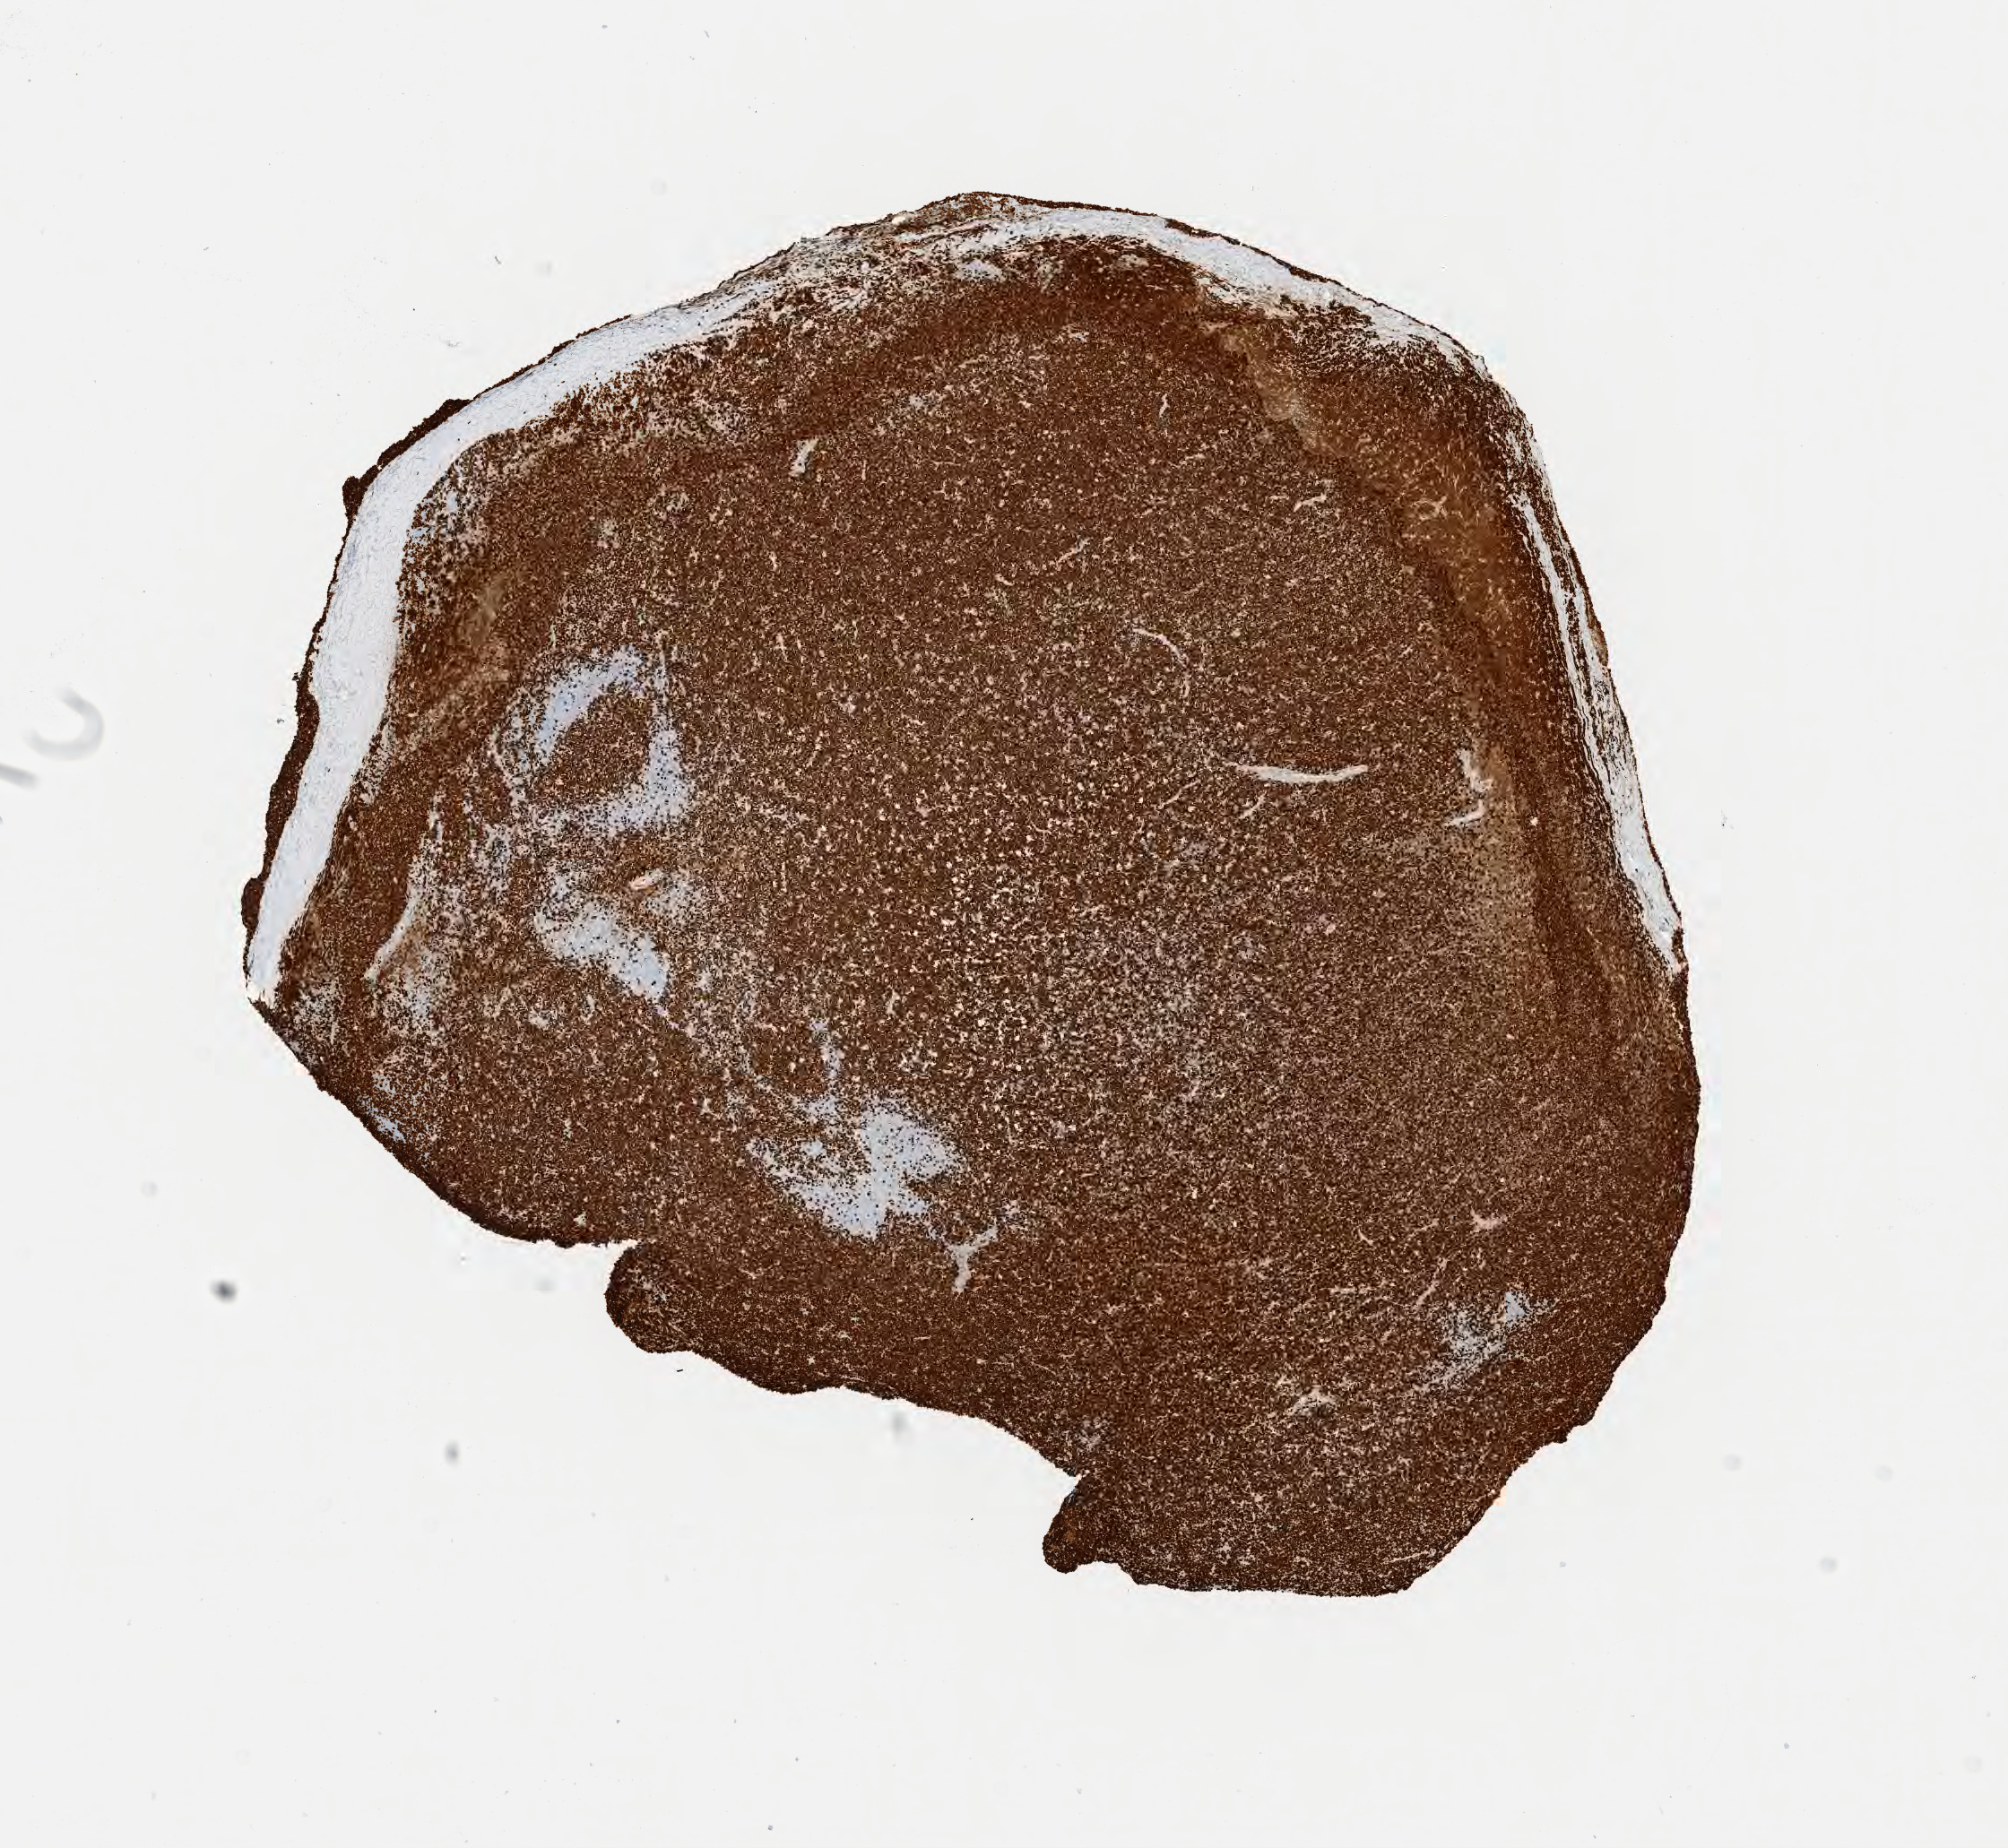
IHC for Ki-67, whole-slide image — a low-resolution overview of the entire scanned area, about 9.1 x 8.3 mm, specimen: tumor tissue. Male patient, age 45 years.
Histologic diagnosis: Burkitt lymphoma, NOS.